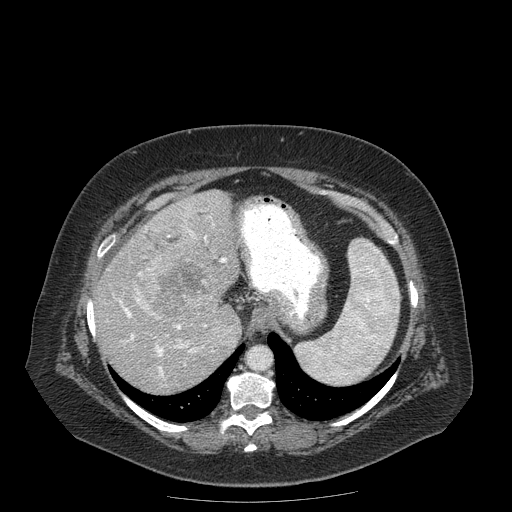
Contrast-enhanced abdominal CT (liver protocol), one axial slice; slice 135 of 204 in the series (ordered by position); reconstruction kernel STANDARD; 120 kVp; soft-tissue window (W 400 / L 40 HU); 2.5 mm slice thickness; 512 × 512 image matrix, field of view 440 × 440 mm. From the clinical record (not read from this slice): diagnosis: hepatocellular carcinoma (patient treated with transarterial chemoembolisation; whether this scan precedes or follows treatment is not stated here); TNM stage (as recorded): Stage-IIIB; Child-Pugh class: A; tumour differentiation: well differentiated; tumour nodularity: uninodular.
Outlined on this slice (semi-automatic segmentation, software-assisted and operator-edited):
- abdominal aorta: bounding box (x1, y1, x2, y2) in pixels: (247, 346, 271, 369)
- liver parenchyma outside the tumour (the mass and vessels are separate outlines, so this box may not span the whole liver): (96, 190, 242, 392)
- mass: (143, 245, 224, 317)
- liver vessels: (119, 216, 227, 377)